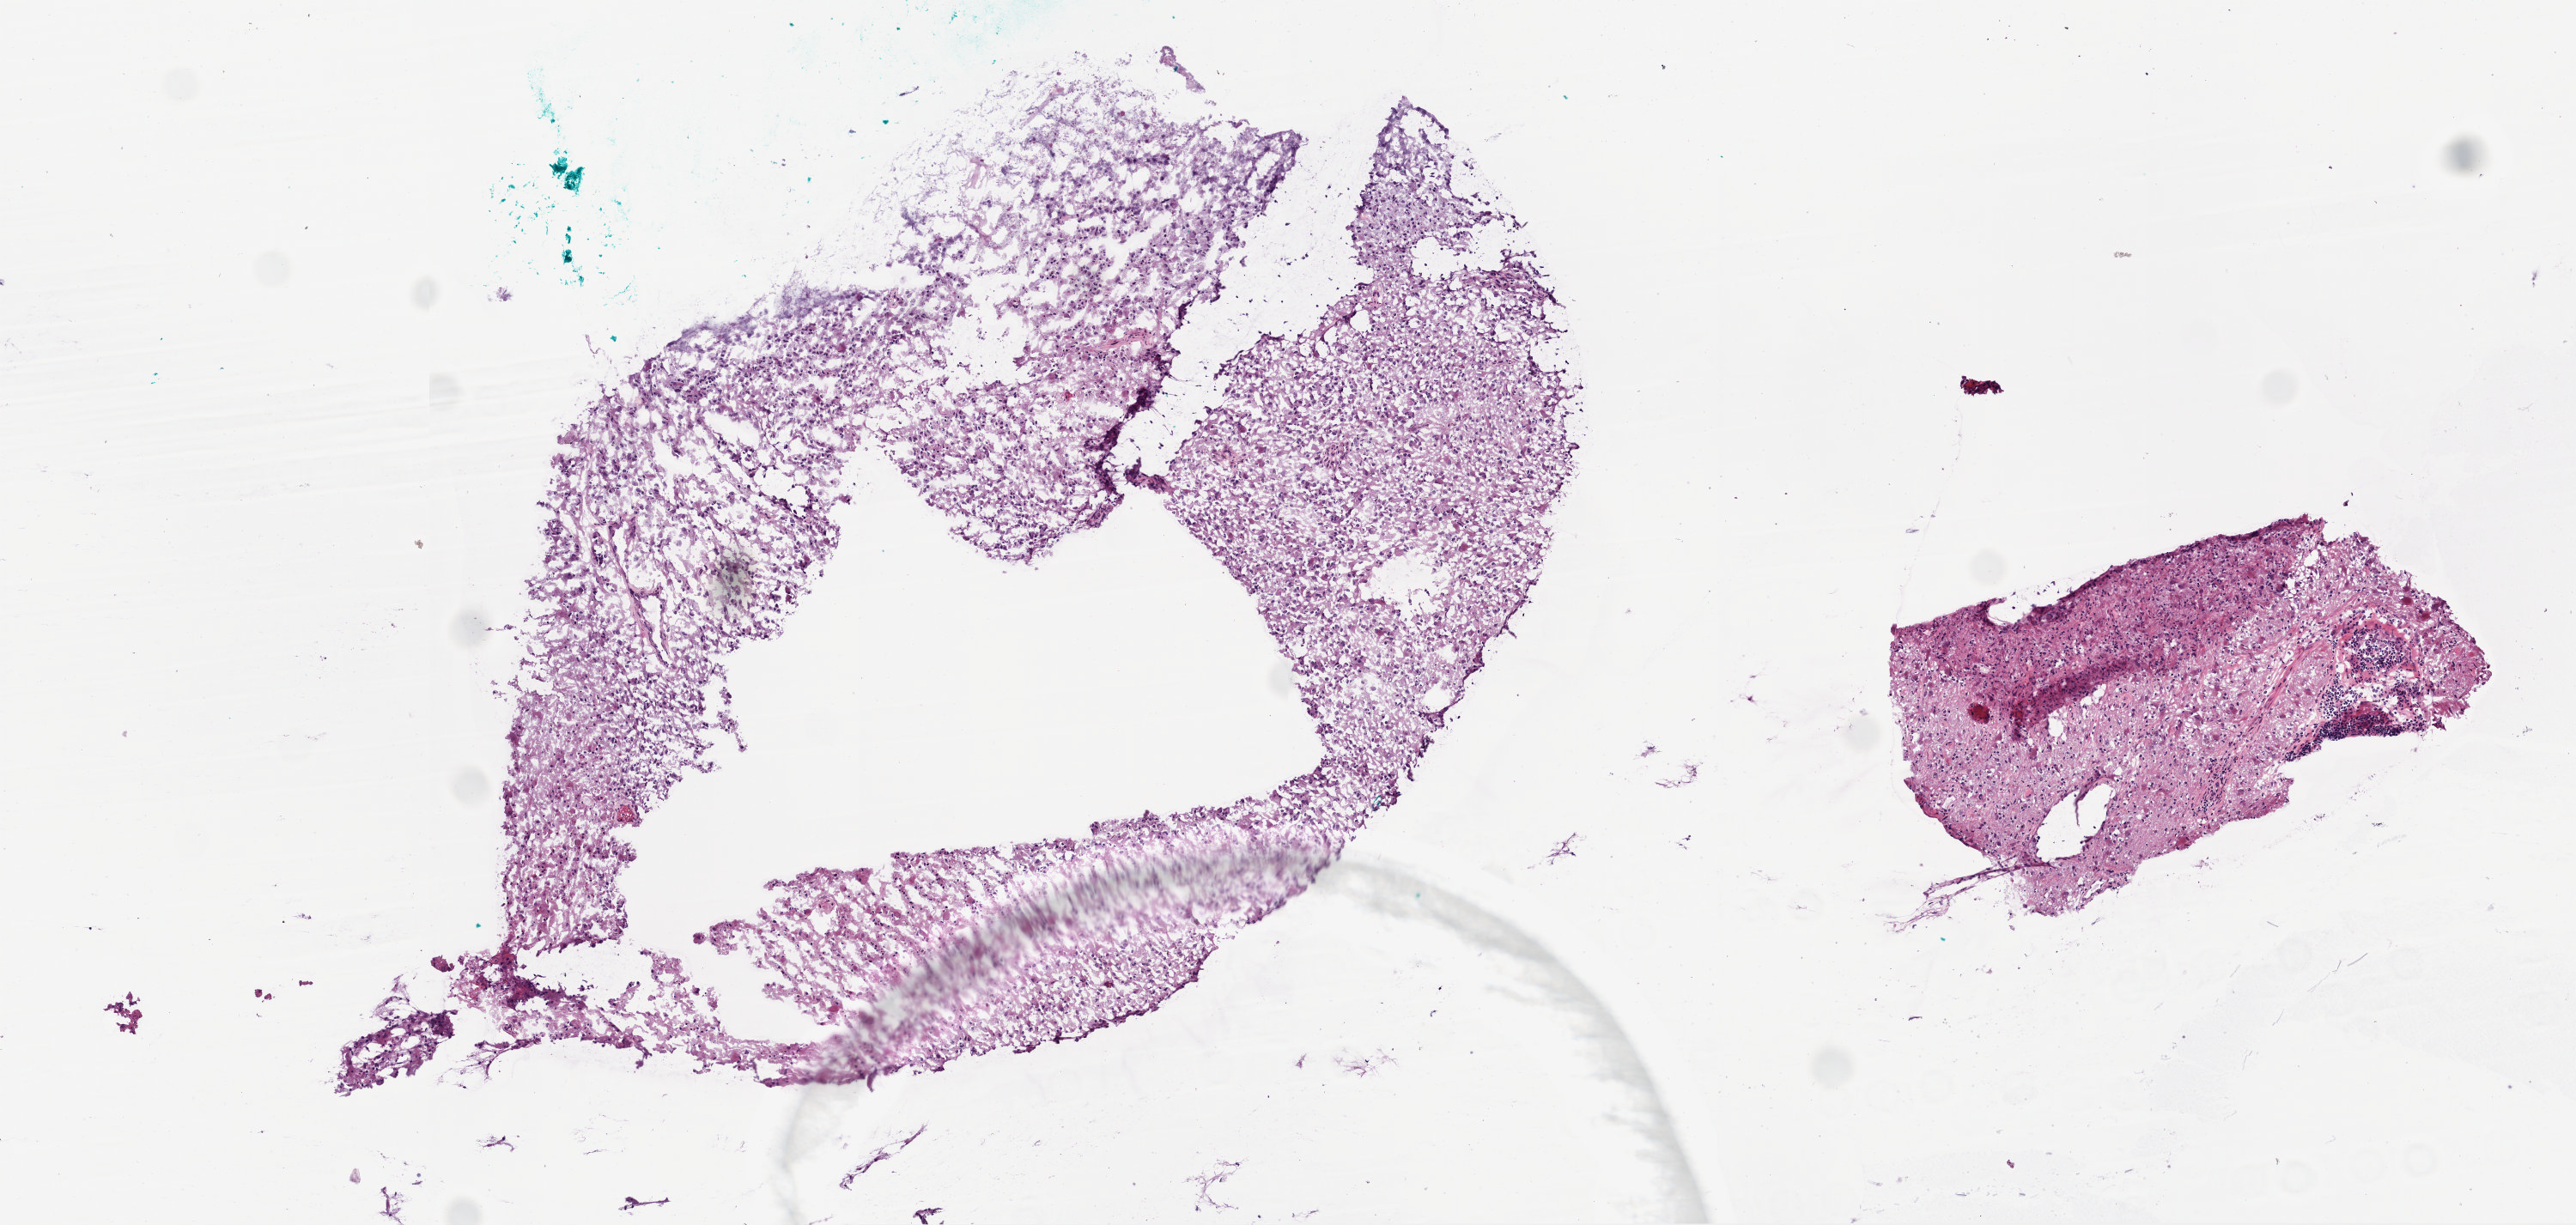
Hematoxylin and eosin (H&E) stained whole-slide image — low-resolution overview of the scanned area, about 6.0 x 2.9 mm (slide scanned at 20x). Composition of this section per pathologist review: tumour cells 70%, tumour nuclei 70%, normal cells 0%, stromal cells 20%, necrosis 10%. Inflammatory infiltration, as recorded: lymphocyte infiltration 100%.
- specimen: frozen section; brain, primary tumour sample